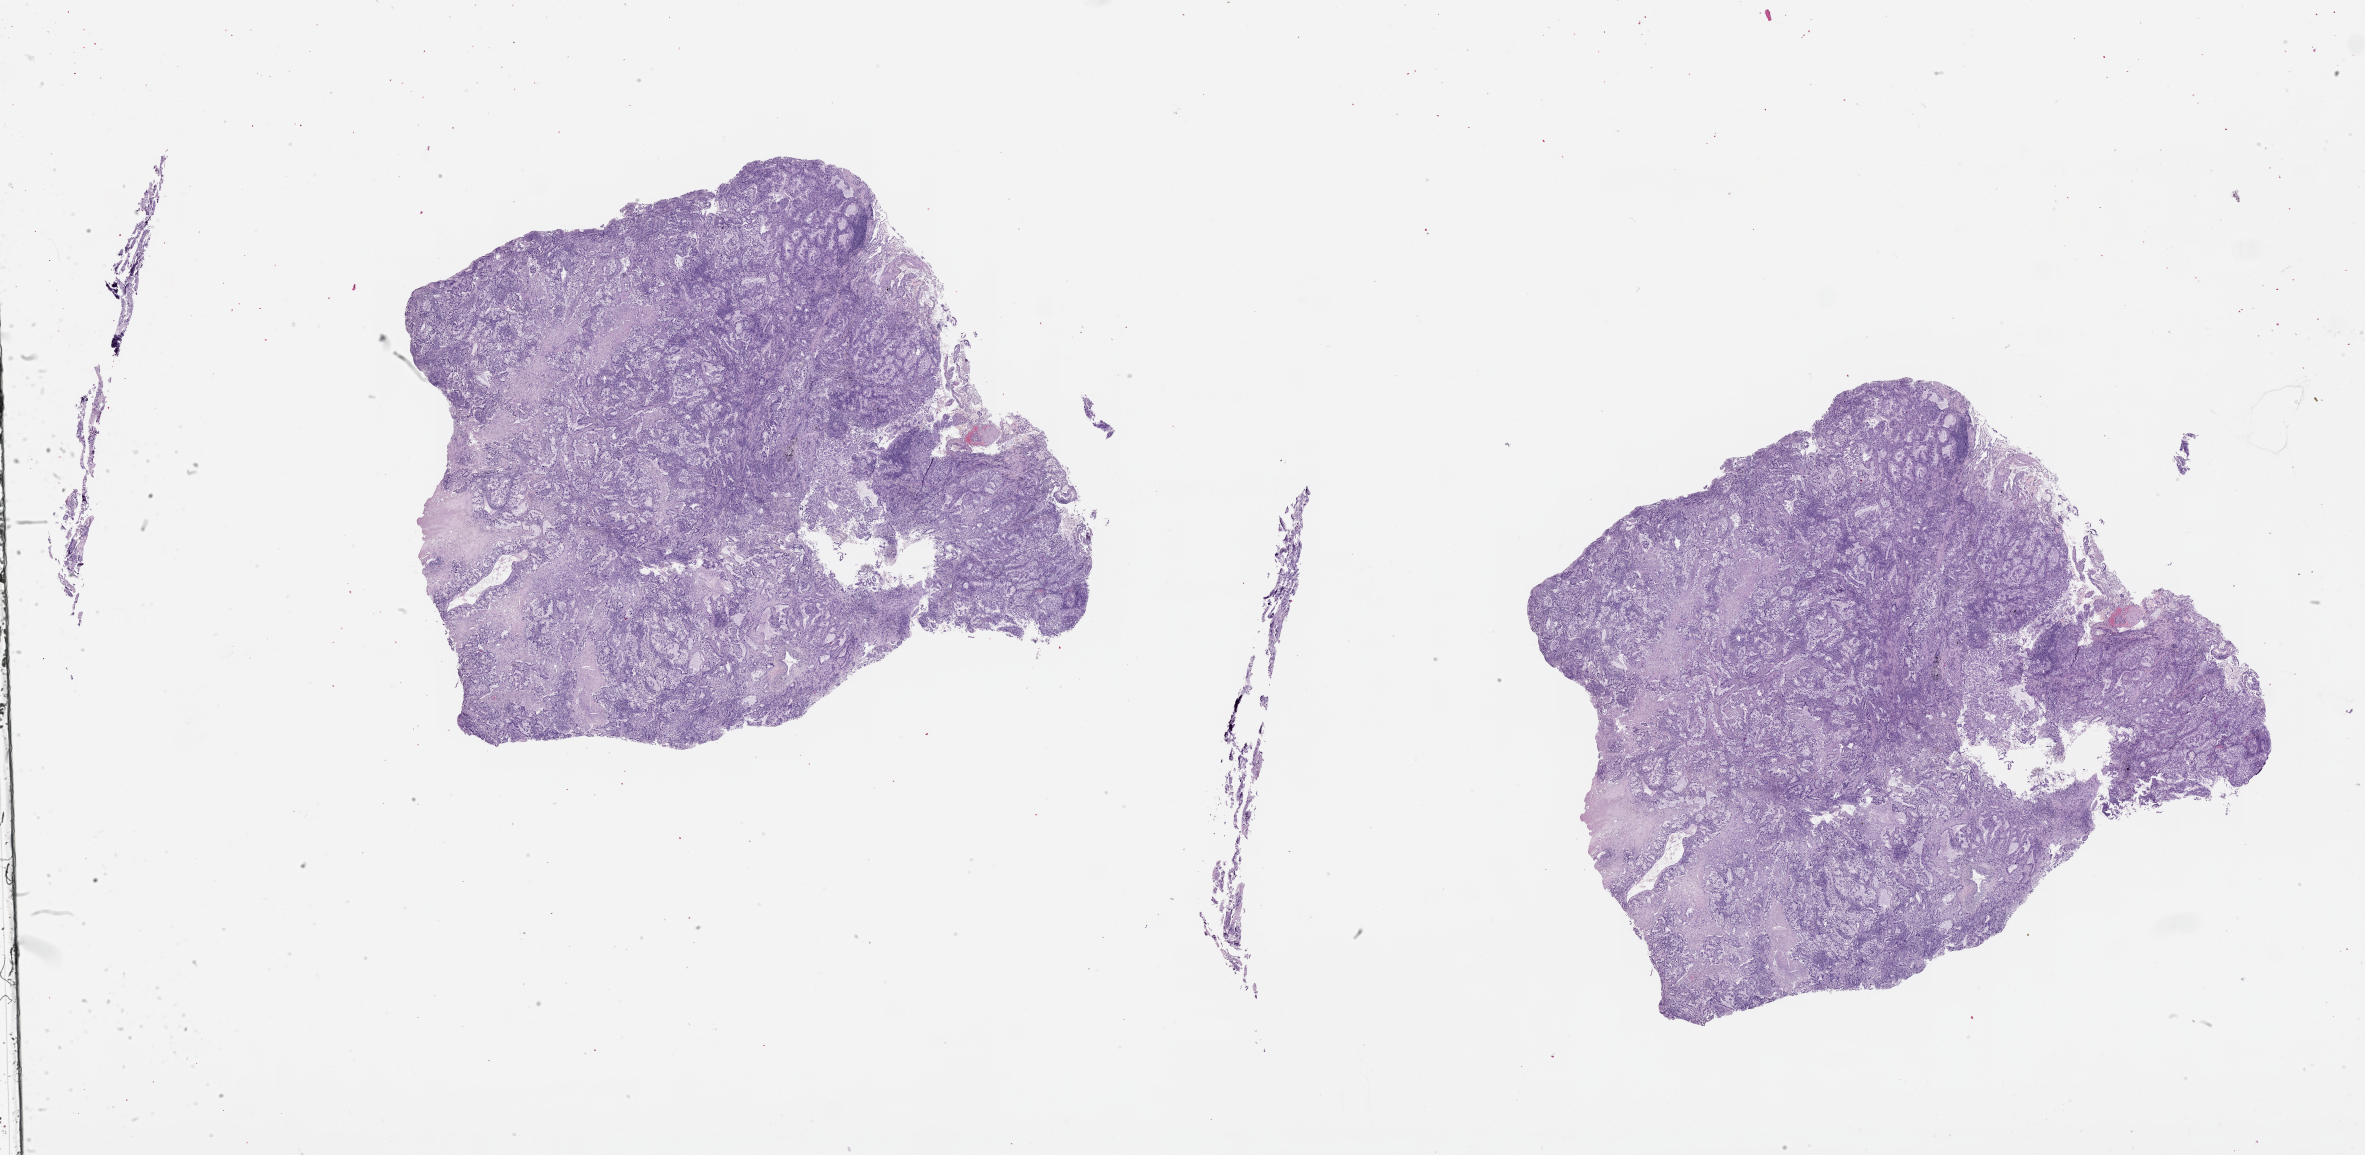
H&E-stained whole-slide image, shown as a low-resolution overview of the whole scanned area (about 38.1 x 18.6 mm); tumour tissue sample, lung. 67-year-old male patient.
Histologic diagnosis: Adenocarcinoma, NOS.